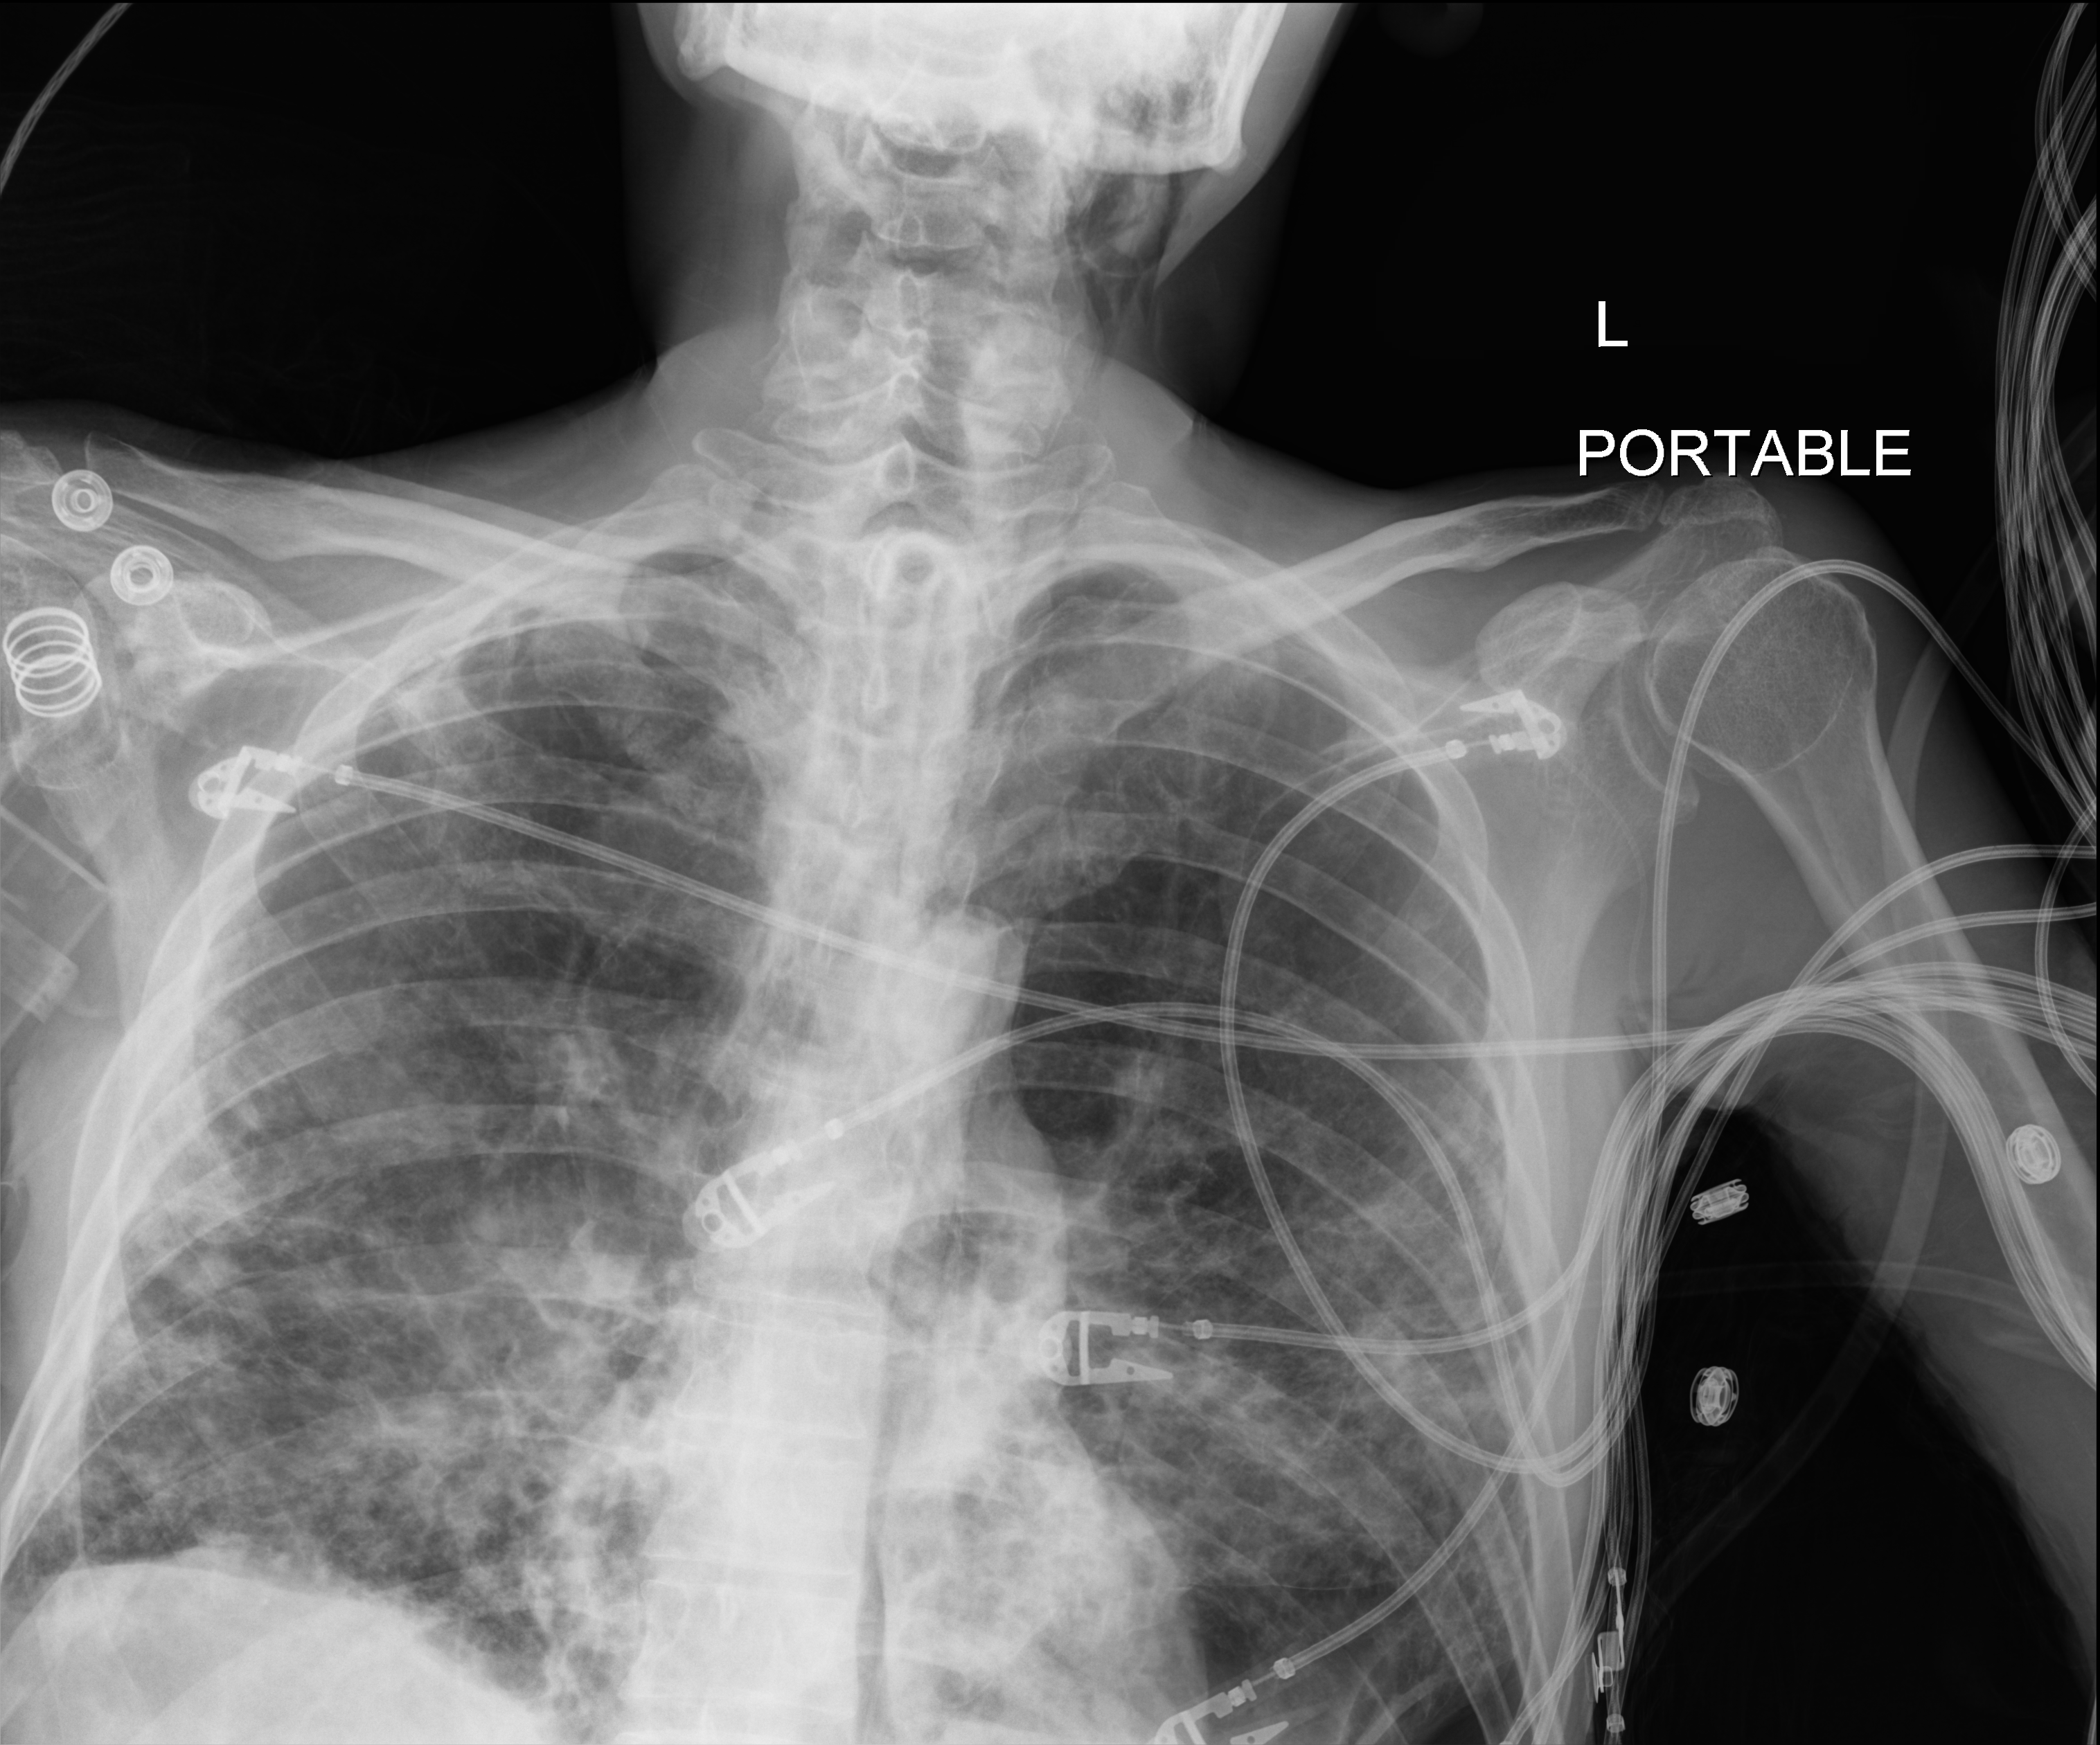
Chest radiograph. Male patient hospitalised with COVID-19, age 18–59 years.
Hospital-stay facts (about this admission, not read from this image; timing relative to this image not recorded):
- mechanically ventilated during this hospital stay: yes
- length of hospital stay: 96 days
- diabetes (admission record): yes